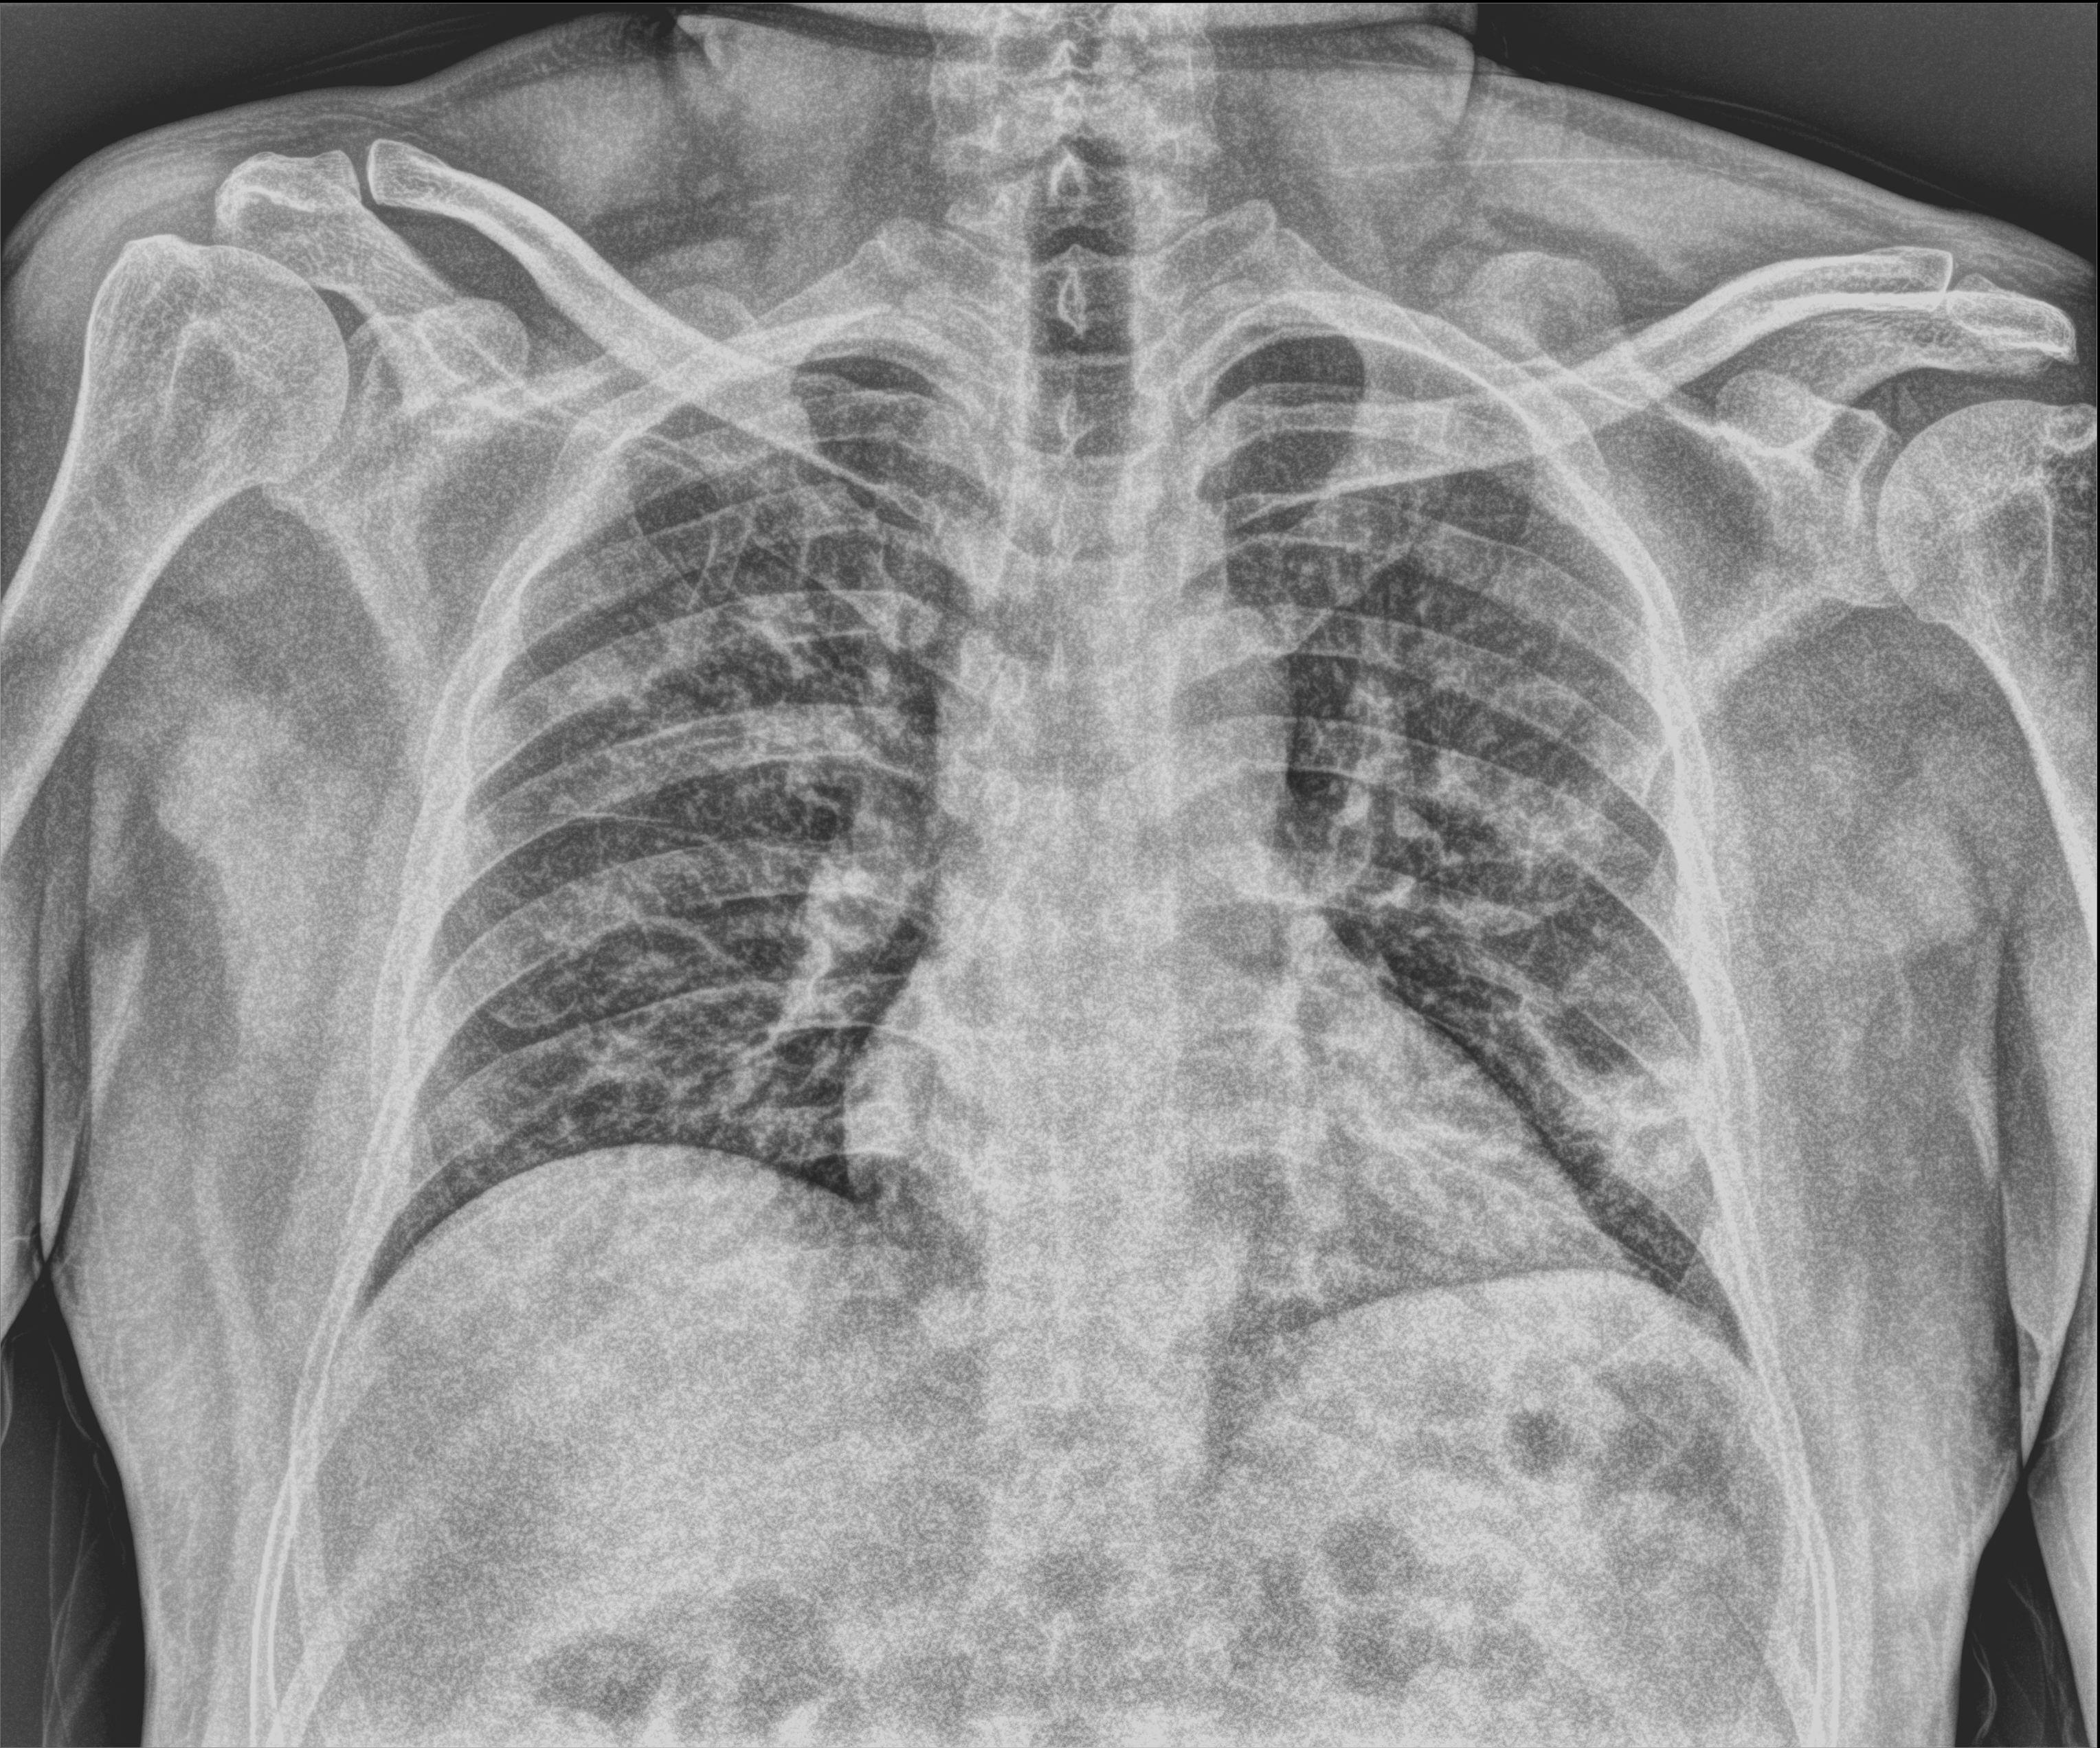
Bedside chest radiograph (computed radiography); anteroposterior (AP) projection. Patient hospitalised with COVID-19; male, aged 18–59 years.
Admission-level facts for this patient (not findings on this image; timing relative to this image not recorded):
- mechanically ventilated during this hospital stay: no